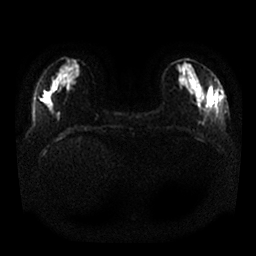
Breast MRI, one axial slice. Position 8 of 25 along the scan axis. Diffusion-weighted series; image 2 of 4 stored at this slice position (different b-values; order by instance number). 1.5 T. 4 mm slice thickness. 256 × 256 image matrix. Female patient.
Annotated regions visible in this slice (outlined manually by an expert reader):
- tumour on diffusion-weighted imaging: bounding box [x1, y1, x2, y2] px = [209, 86, 222, 108]